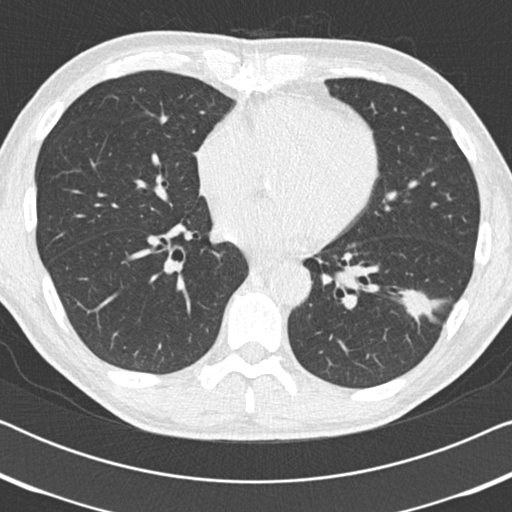
Chest CT (low-dose screening protocol), one axial image; third screening round (two years after baseline); lung window (W 1500 / L -600 HU); 2 mm slice thickness. Male participant, aged 59 years at enrolment. Current smoker at enrolment.
Expert reader's lesion annotation, bounding box (x1, y1, x2, y2) in pixels: (388, 274, 456, 336). The screening reader recorded 2 non-calcified nodules or masses ≥4 mm on this exam; which of them this box marks is not recorded. Official screen result: positive, other. Later outcome: lung cancer diagnosed 73 days after this screen — adenocarcinoma, NOS, left lower lobe, poorly differentiated (G3), stage IA (AJCC 6th edition), 20 mm at pathology.